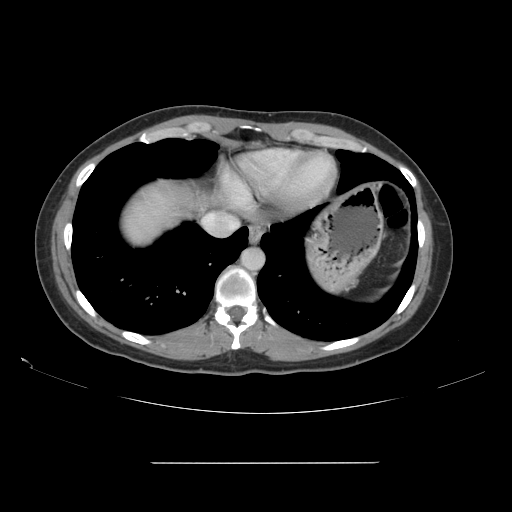
Contrast-enhanced abdominal CT, one axial slice; position 140 of 151 along the scan axis; intravenous contrast given; soft-tissue window (W 400 / L 40 HU); 2.5 mm slice thickness; 512 × 512 image matrix, field of view 421 × 421 mm. Female patient, age 46 years. From the clinical record (not read from this slice): diagnosis: colorectal cancer liver metastases, imaged before liver resection.
Annotated regions visible in this slice (outlined manually by an expert reader):
- liver: bounding box (x1, y1, x2, y2) in pixels: (134, 197, 168, 228)
- planned liver remnant (the part of the liver to remain after resection): (147, 197, 172, 213)